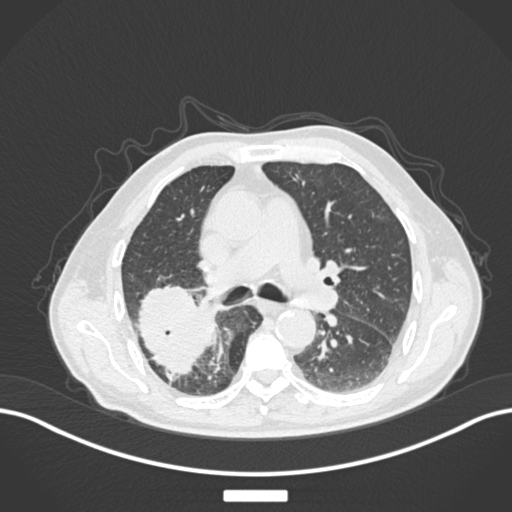
Chest CT, one axial slice; slice 104 of 201 in the series (ordered by position); 120 kVp; lung window (W 1500 / L -600 HU); 1 mm slice thickness; 512 × 512 image matrix. Patient: male, 72 years. From the clinical record (not read from this slice): clinical TNM (as recorded): T3 N2 M0.
Structures marked on this image (bounding box drawn by a radiologist):
- lung tumour (recorded histology: adenocarcinoma): box from (x=132, y=281) to (x=214, y=379) px